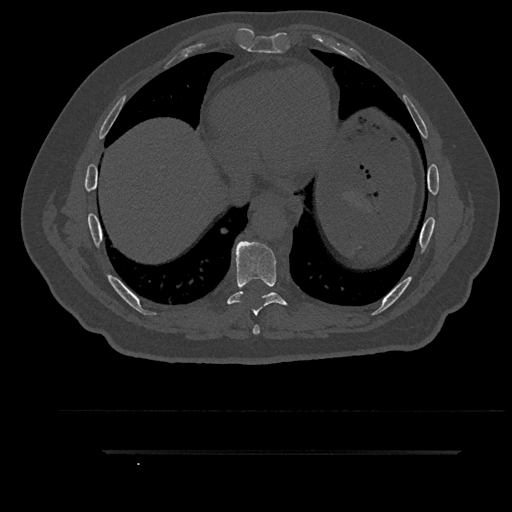
CT including the spine, one axial slice. Position 475 of 797 along the scan axis. 120 kVp. Bone window (W 1800 / L 400 HU). 512 × 512 image matrix, field of view 432 × 432 mm. Patient: male, 63 years. Case-level facts recorded for this patient, not image findings: primary cancer: renal.
Outlined on this slice (semi-automatic segmentation, software-assisted and operator-edited):
- T7 vertebra: bounding box [x1, y1, x2, y2] px = [253, 325, 260, 335]
- T8 vertebra: [221, 241, 293, 316]